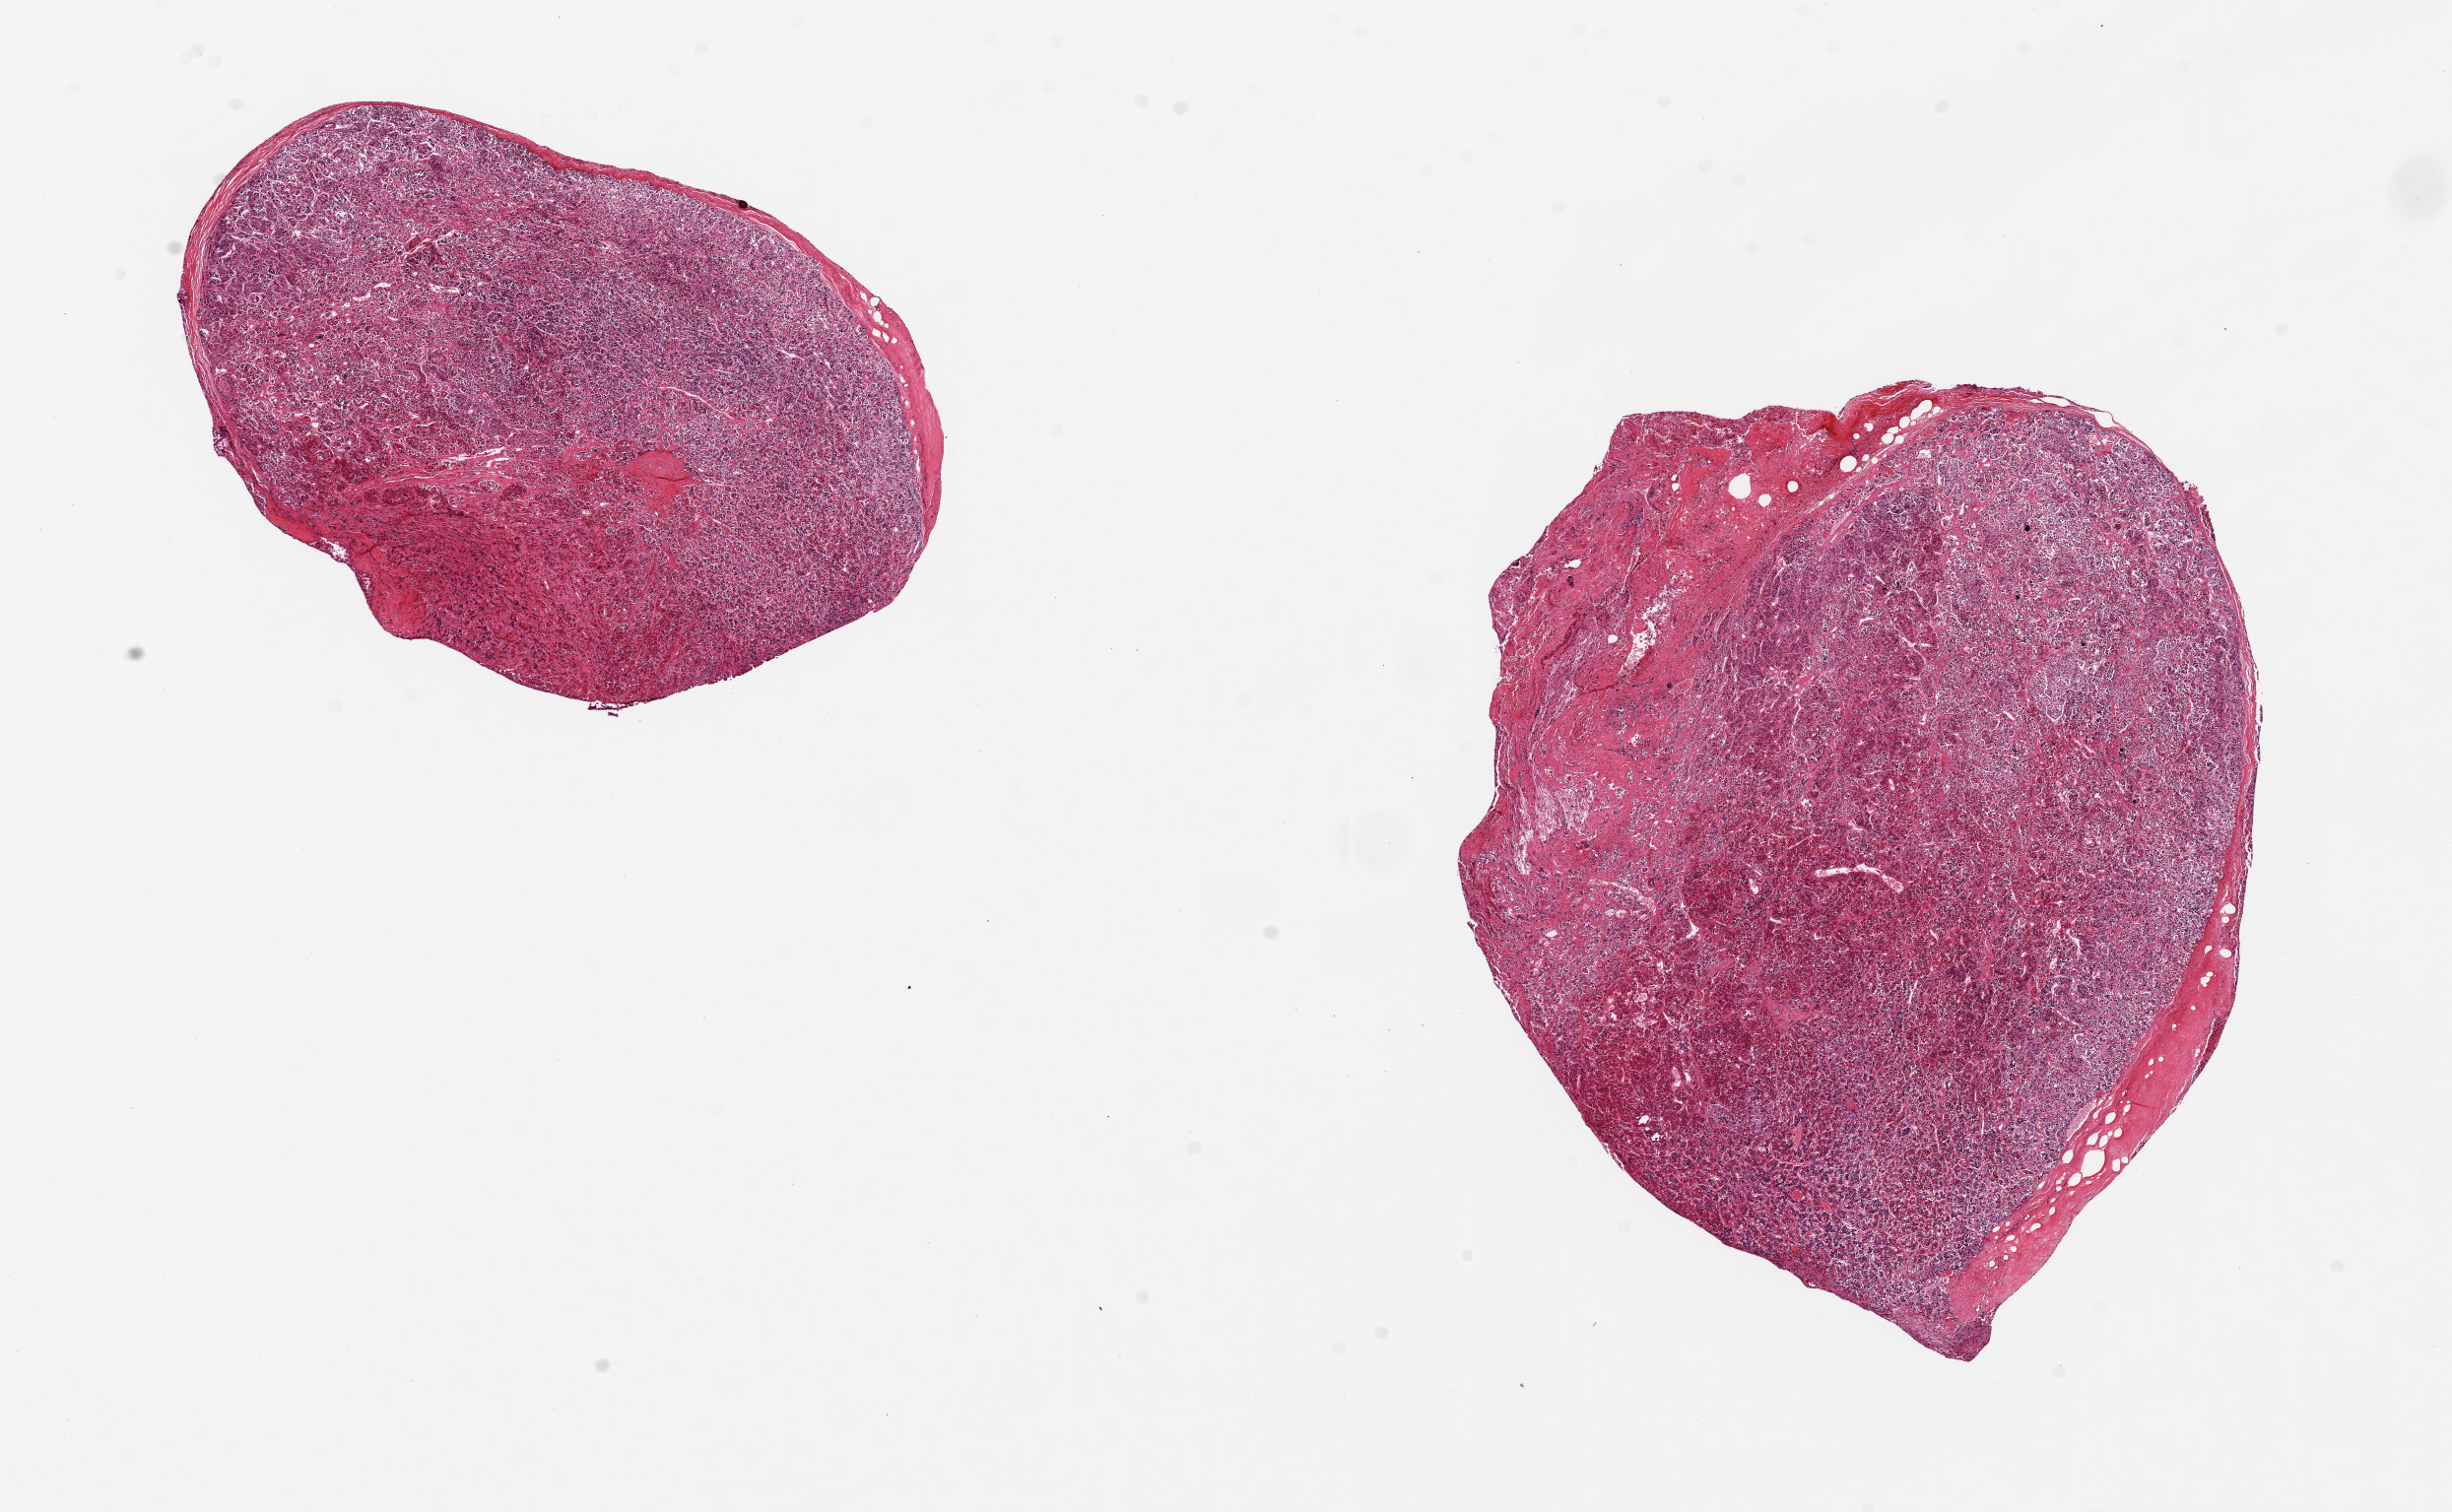
Digitized H&E-stained section — a low-resolution overview of the entire scanned area, about 19.7 x 12.1 mm; PAXgene-fixed paraffin-embedded (PFPE) section; sampled site (target tissue): pituitary; donor tissue sample. Donor sex: male.
Reviewer comment on this tissue sample: 2 pieces, 6x4 & 8x7mm; anterior pituitary.